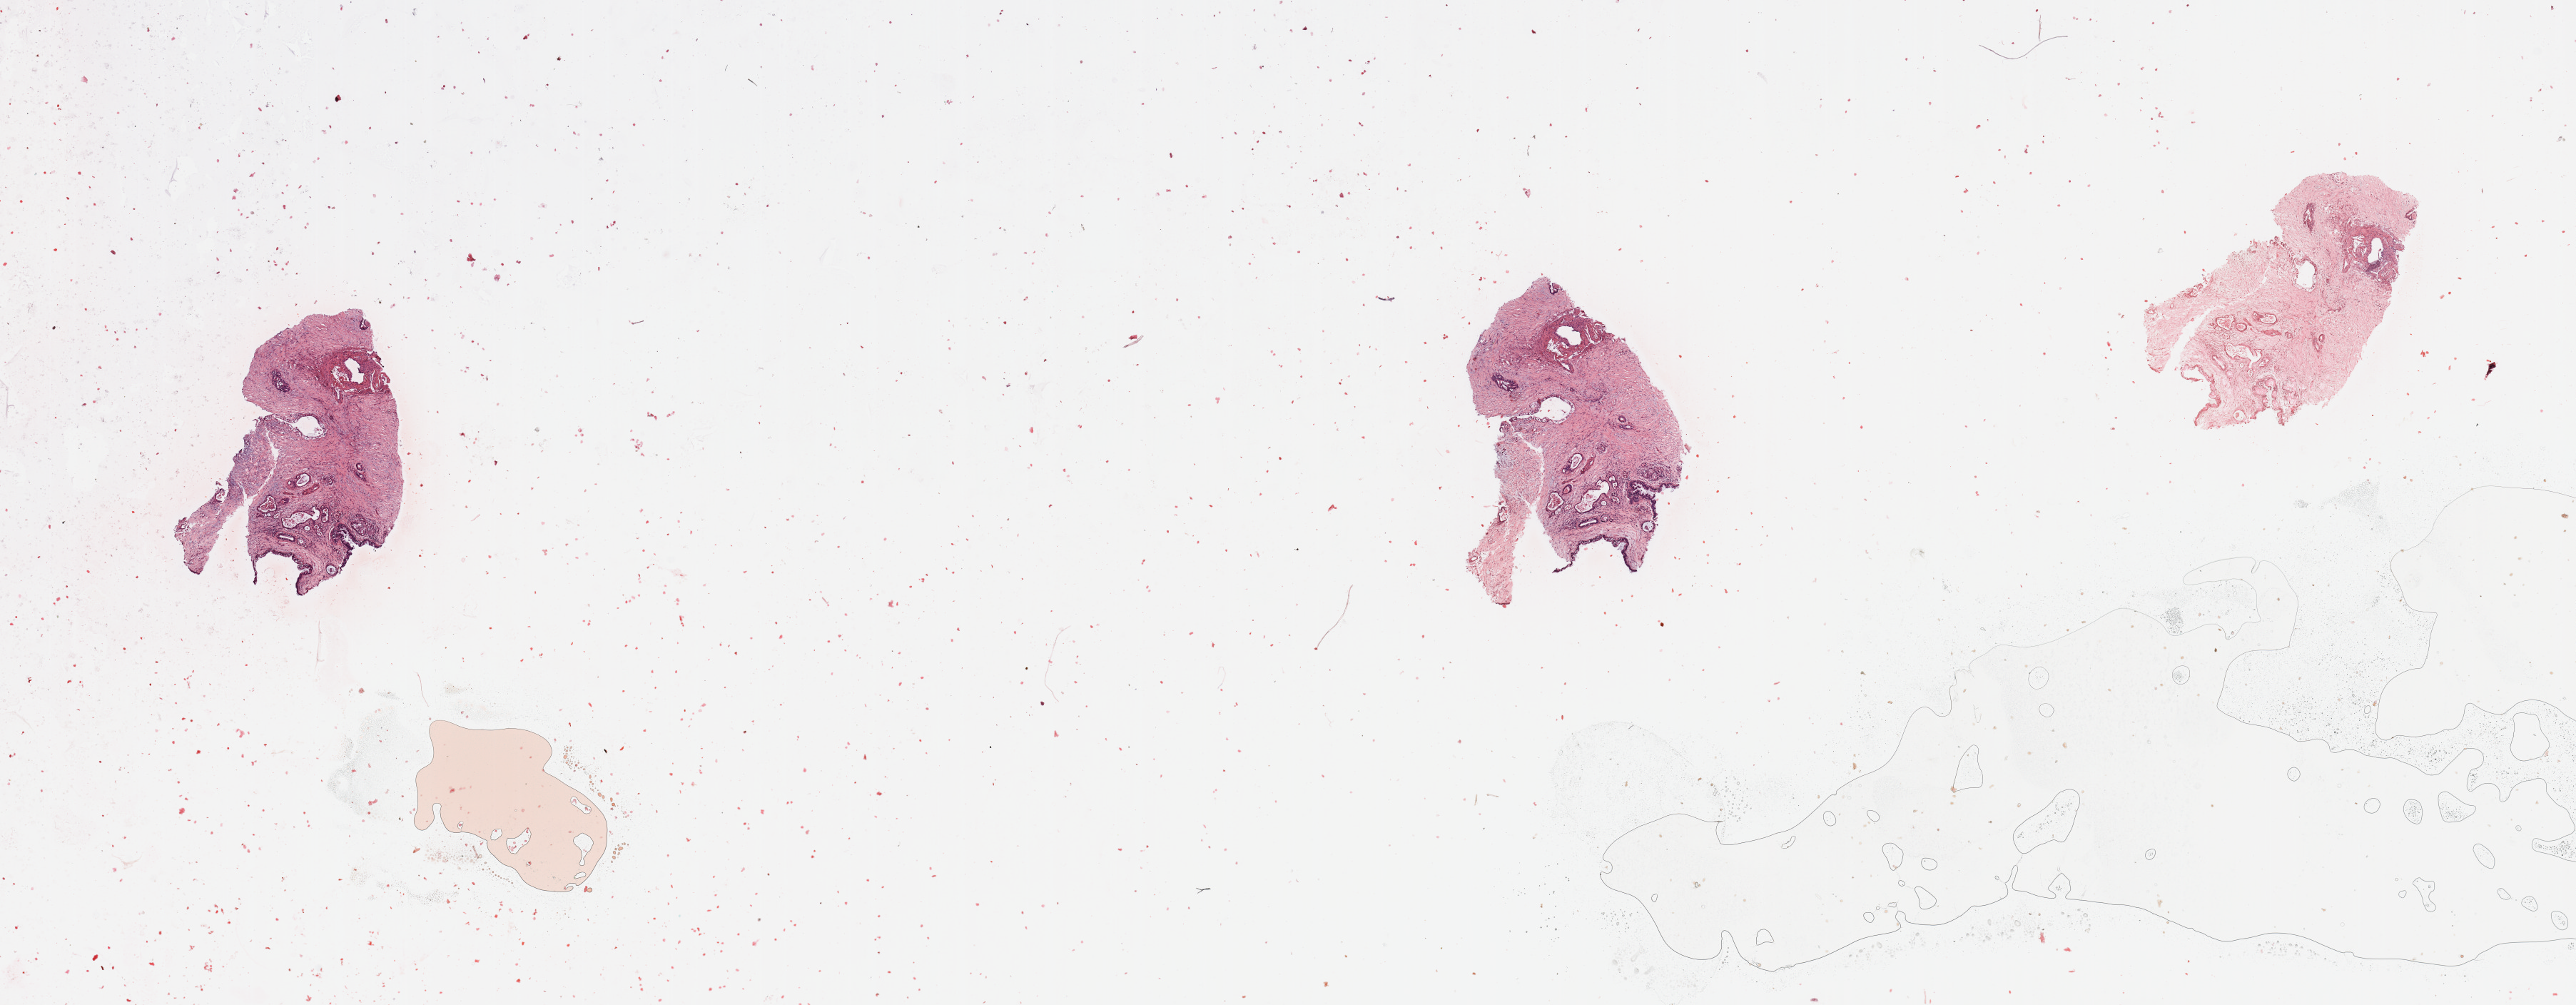
H&E whole-slide image — low-resolution overview of the scanned area, about 28.5 x 11.1 mm; tumour tissue sample, sampled site: pancreas. Patient: female, age 77 years. Histologic grade: G2 (moderately differentiated). Slide review estimates, as recorded: tumour nuclei 10%, necrosis 2%.
Primary tumour site (as recorded): head. Histologic diagnosis: Infiltrating duct carcinoma, NOS. AJCC pathologic stage: IIB.